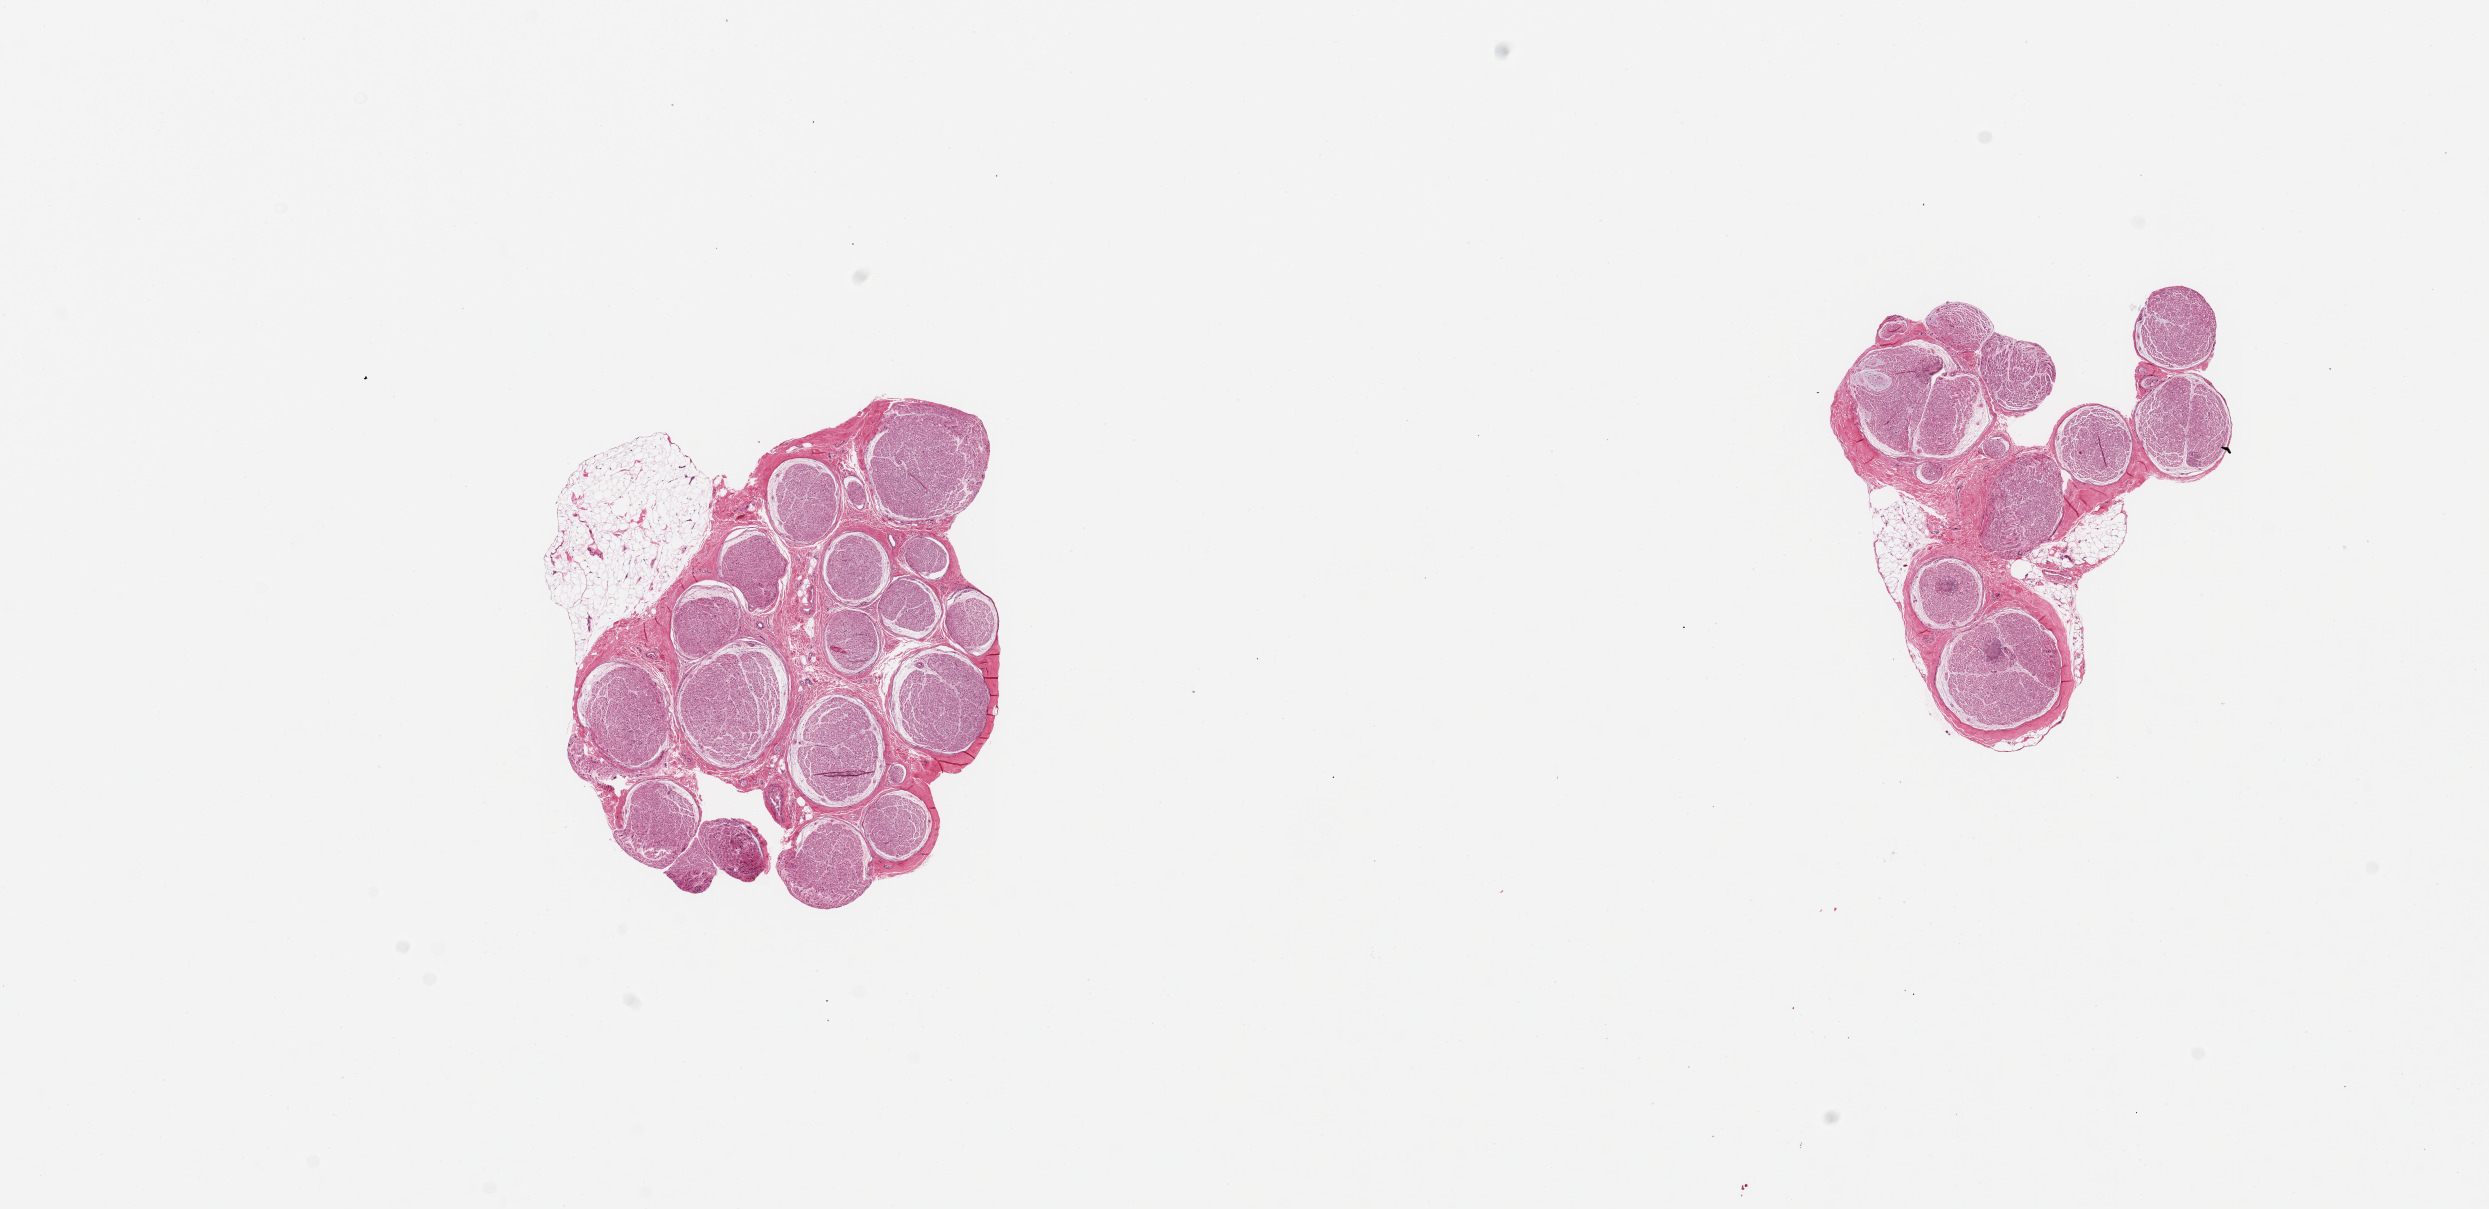
Digitized H&E-stained section, whole scanned area (about 19.7 x 9.6 mm, from a 20x scan) shown as a low-resolution overview, PAXgene-fixed, paraffin-embedded tissue, target tissue: tibial nerve, donor tissue sample. Donor sex: female.
Pathologist's review note for this sample: 2 pieces, 4x4 & 3.5x3mm; Imm nubbin adheren fat on one, otherwise clean.